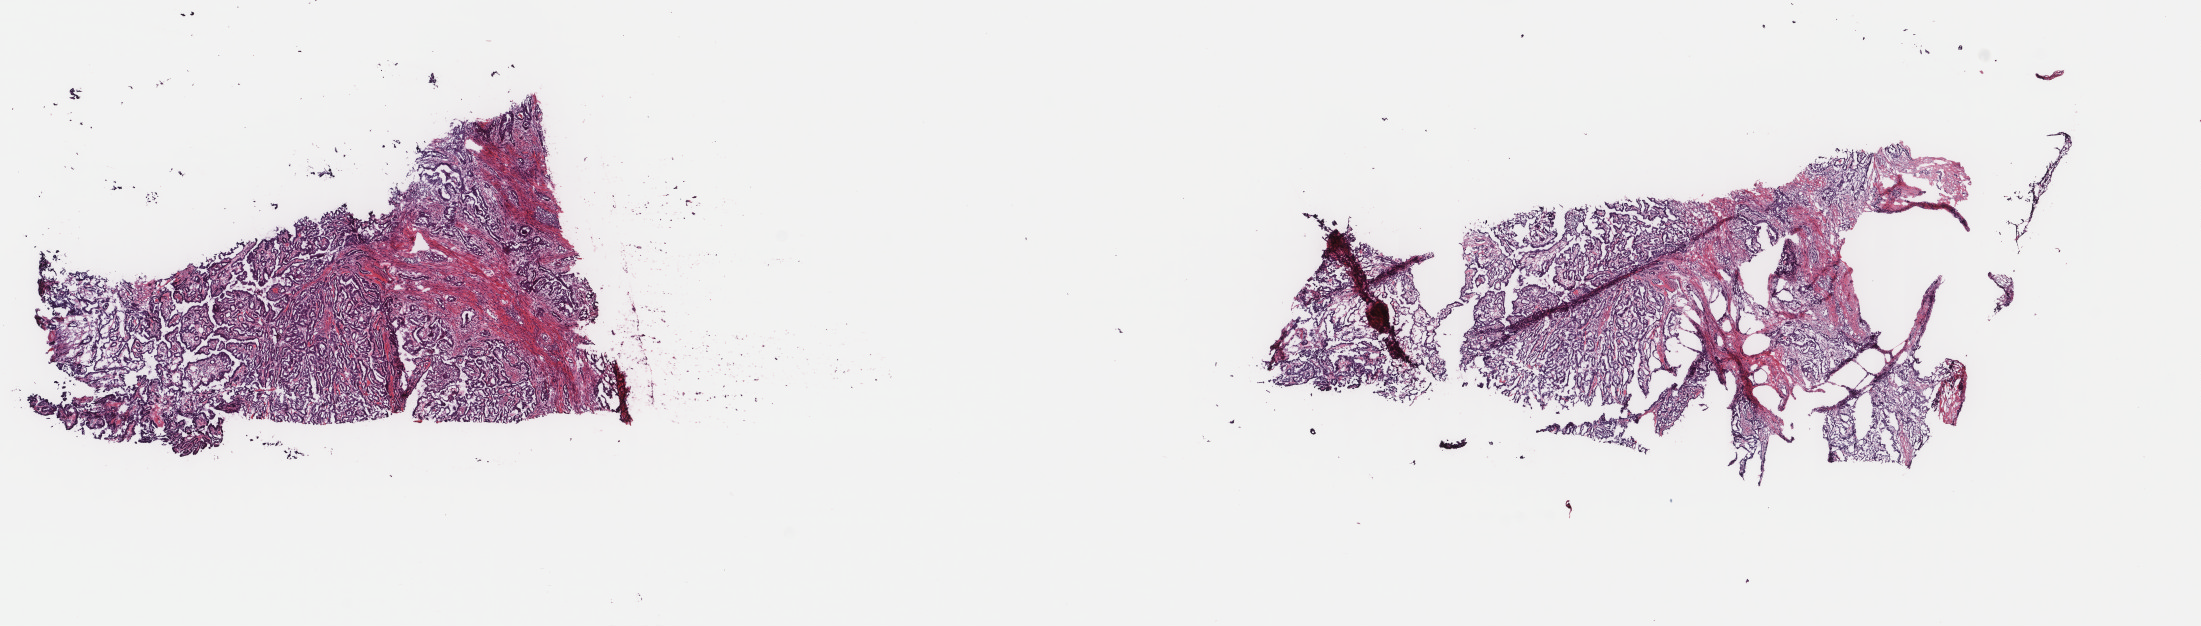
Whole-slide histology image, H&E, a low-resolution overview of the entire scanned area, about 17.5 x 5.0 mm, frozen section, thyroid, primary tumour sample. Female, age 46 years at initial diagnosis. Composition of this section per pathologist review: tumour cells 95%, tumour nuclei 80%, normal cells 0%, stromal cells 5%, necrosis 0%. Infiltration values recorded for this section: lymphocyte infiltration 0%, monocyte infiltration 0%, neutrophil infiltration 0%.
TNM: T3 N1a M0. Diagnosis: Papillary carcinoma, columnar cell (thyroid gland). Laterality: bilateral. AJCC pathologic stage: III. Lymph nodes positive (case pathology): 1 of 2 examined.